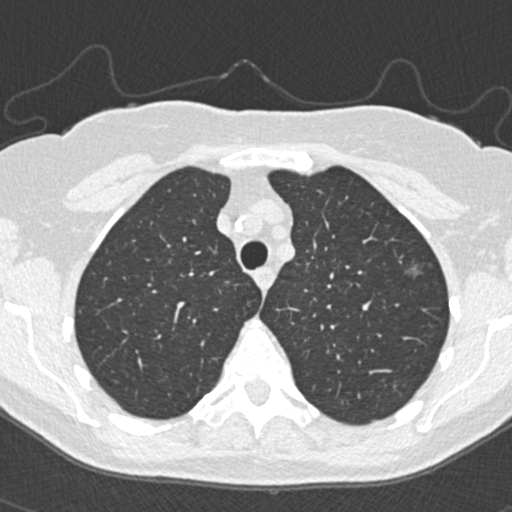
Low-dose screening chest CT, one axial slice. Position 284 of 350 along the scan axis. Reconstruction kernel B30f. 120 kVp. Lung window (W 1500 / L -600 HU). 512 × 512 image matrix.
Structures marked on this image (expert manual segmentation):
- lesion 3 (tumor, upper lobe of left lung): bounding box <408,265,421,278> (left, top, right, bottom; pixels)